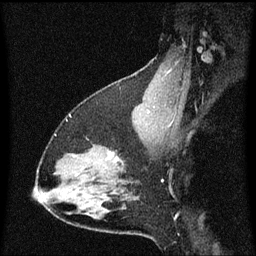
Breast MRI (dynamic contrast-enhanced), one sagittal slice. Slice 42 of 60 in the series (ordered by position). Dynamic contrast-enhanced series, image 2 of 3 at this slice position (ordered by acquisition). 1.5 T. TE 4.2 ms, TR 8.4 ms. 256 × 256 image matrix, field of view 200 × 200 mm. Female patient, age 38 years. Case-level facts recorded for this patient, not image findings: setting: breast cancer imaged before/during neoadjuvant chemotherapy; receptor status: HR-positive, HER2-negative.
Outlined on this slice (semi-automatic segmentation, software-assisted and operator-edited):
- analysis volume of interest (the breast-tissue region the enhancement analysis was run in; not a lesion): bounding box <94,144,135,185> (left, top, right, bottom; pixels)
- tumour enhancement mask (voxels above the 70 % enhancement threshold inside the analysis volume of interest): <109,152,120,163>